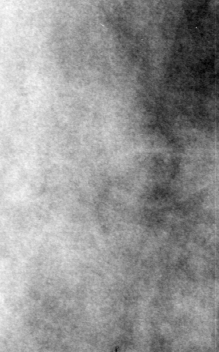
Region of interest cut from a scanned film mammogram (one marked finding); left breast; MLO view.
Marked abnormality: mass, shape focal asymmetric density, margins ill defined; BI-RADS assessment category 3; subtlety rating 1 on a 1 (subtle) to 5 (obvious) scale; pathology result (as recorded, not read from the image): benign.